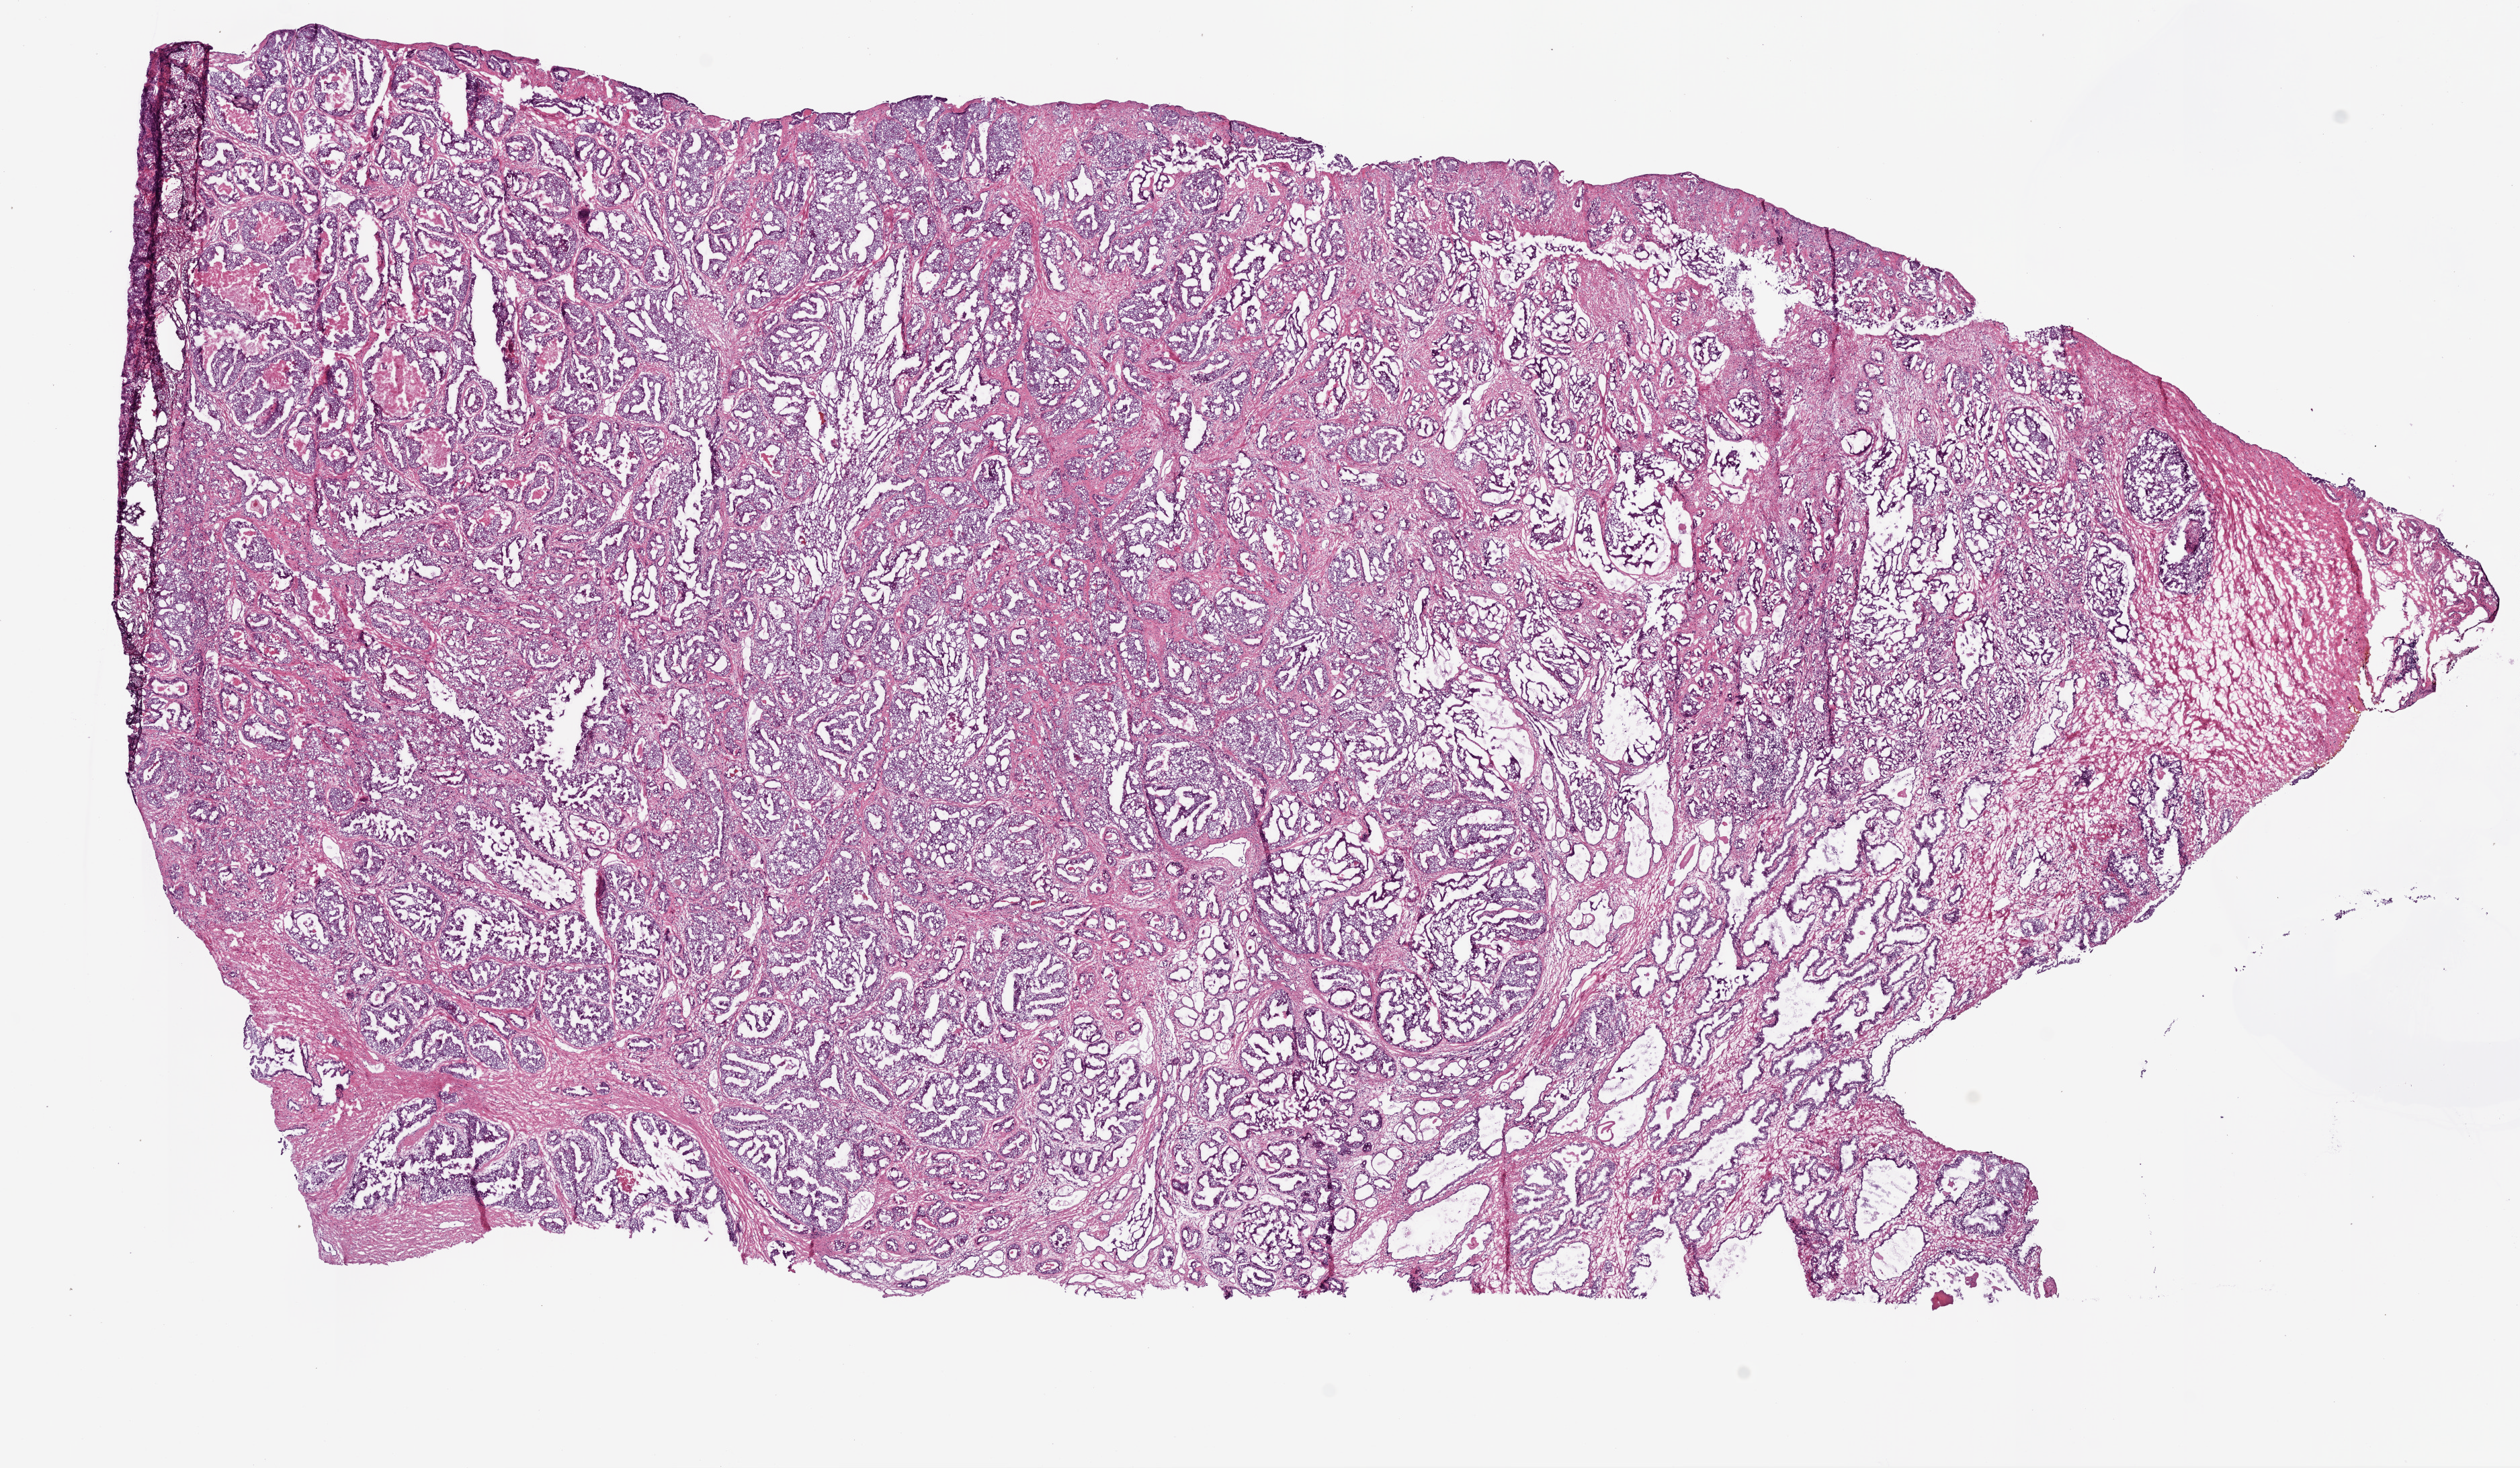
Hematoxylin and eosin (H&E) stained whole-slide image, whole scanned area (about 15.0 x 8.8 mm, acquisition: 20x scan) shown as a low-resolution overview, frozen section from the bottom of the tissue portion, primary tumour sample from the prostate. Male patient; age at initial diagnosis 54 years. Gleason score: 9 (4+5). Composition of this section per pathologist review: tumour cells 55%, tumour nuclei 60%, normal cells 20%, stromal cells 25%, necrosis 5%. Infiltration values recorded for this section: lymphocyte infiltration 2%, monocyte infiltration 3%, neutrophil infiltration 2%.
Lymph nodes positive (case pathology): 2 of 21 examined. Pathologic diagnosis: Acinar cell carcinoma (prostate gland).